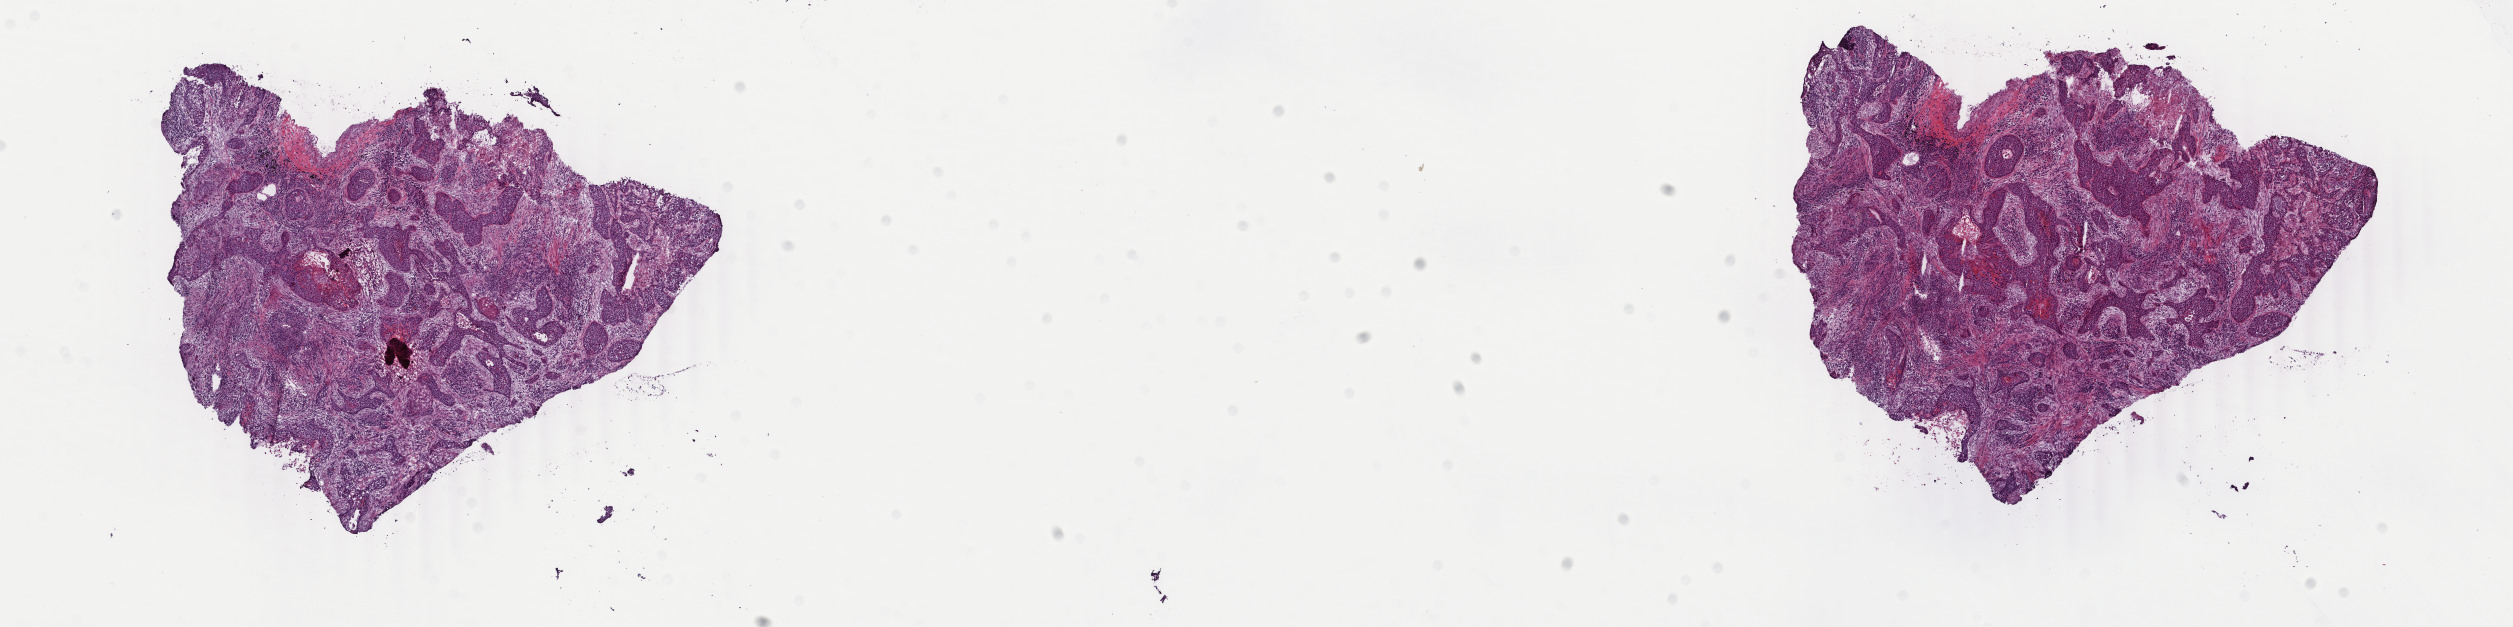
H&E-stained whole-slide image, a low-resolution overview of the entire scanned area, about 20.0 x 5.0 mm (slide scanned at 40x). Frozen section from the top of the tissue portion. Sample: primary tumour, lung. Male, age 78 years at initial diagnosis. Pathologist review of this section (percent, as recorded): tumour cells 70%, tumour nuclei 70%, normal cells 0%, stromal cells 29%, necrosis 1%. Infiltration values recorded for this section: lymphocyte infiltration 7%, monocyte infiltration 2%, neutrophil infiltration 4%.
• TNM: T2 N0 M0
• histologic diagnosis: Squamous cell carcinoma, NOS (upper lobe, lung)
• AJCC pathologic stage: IB (6th edition)